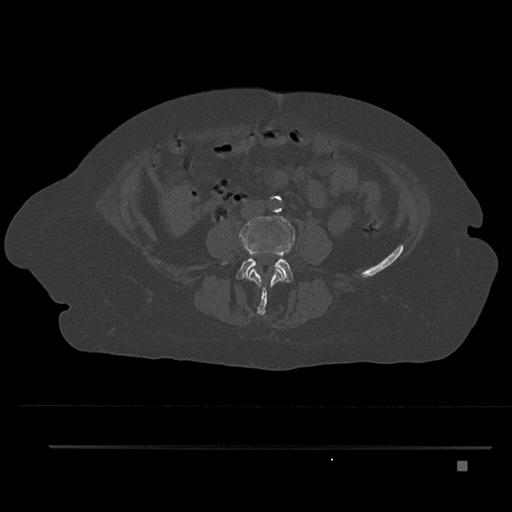
CT including the spine, one axial slice. Position 98 of 797 along the scan axis. Reconstruction kernel Br40s/3. 120 kVp. Bone window (W 1800 / L 400 HU). 0.5 mm slice thickness. 512 × 512 image matrix, field of view 437 × 437 mm. Patient: female, 76 years. Case-level facts recorded for this patient, not image findings: primary cancer: lung; vertebrae with lytic lesions (as recorded): T11, L3.
Outlined on this slice (semi-automatically segmented with operator editing):
- L3 vertebra: box from (x=248, y=266) to (x=285, y=315) px
- L4 vertebra: (x=223, y=216)–(x=296, y=283)